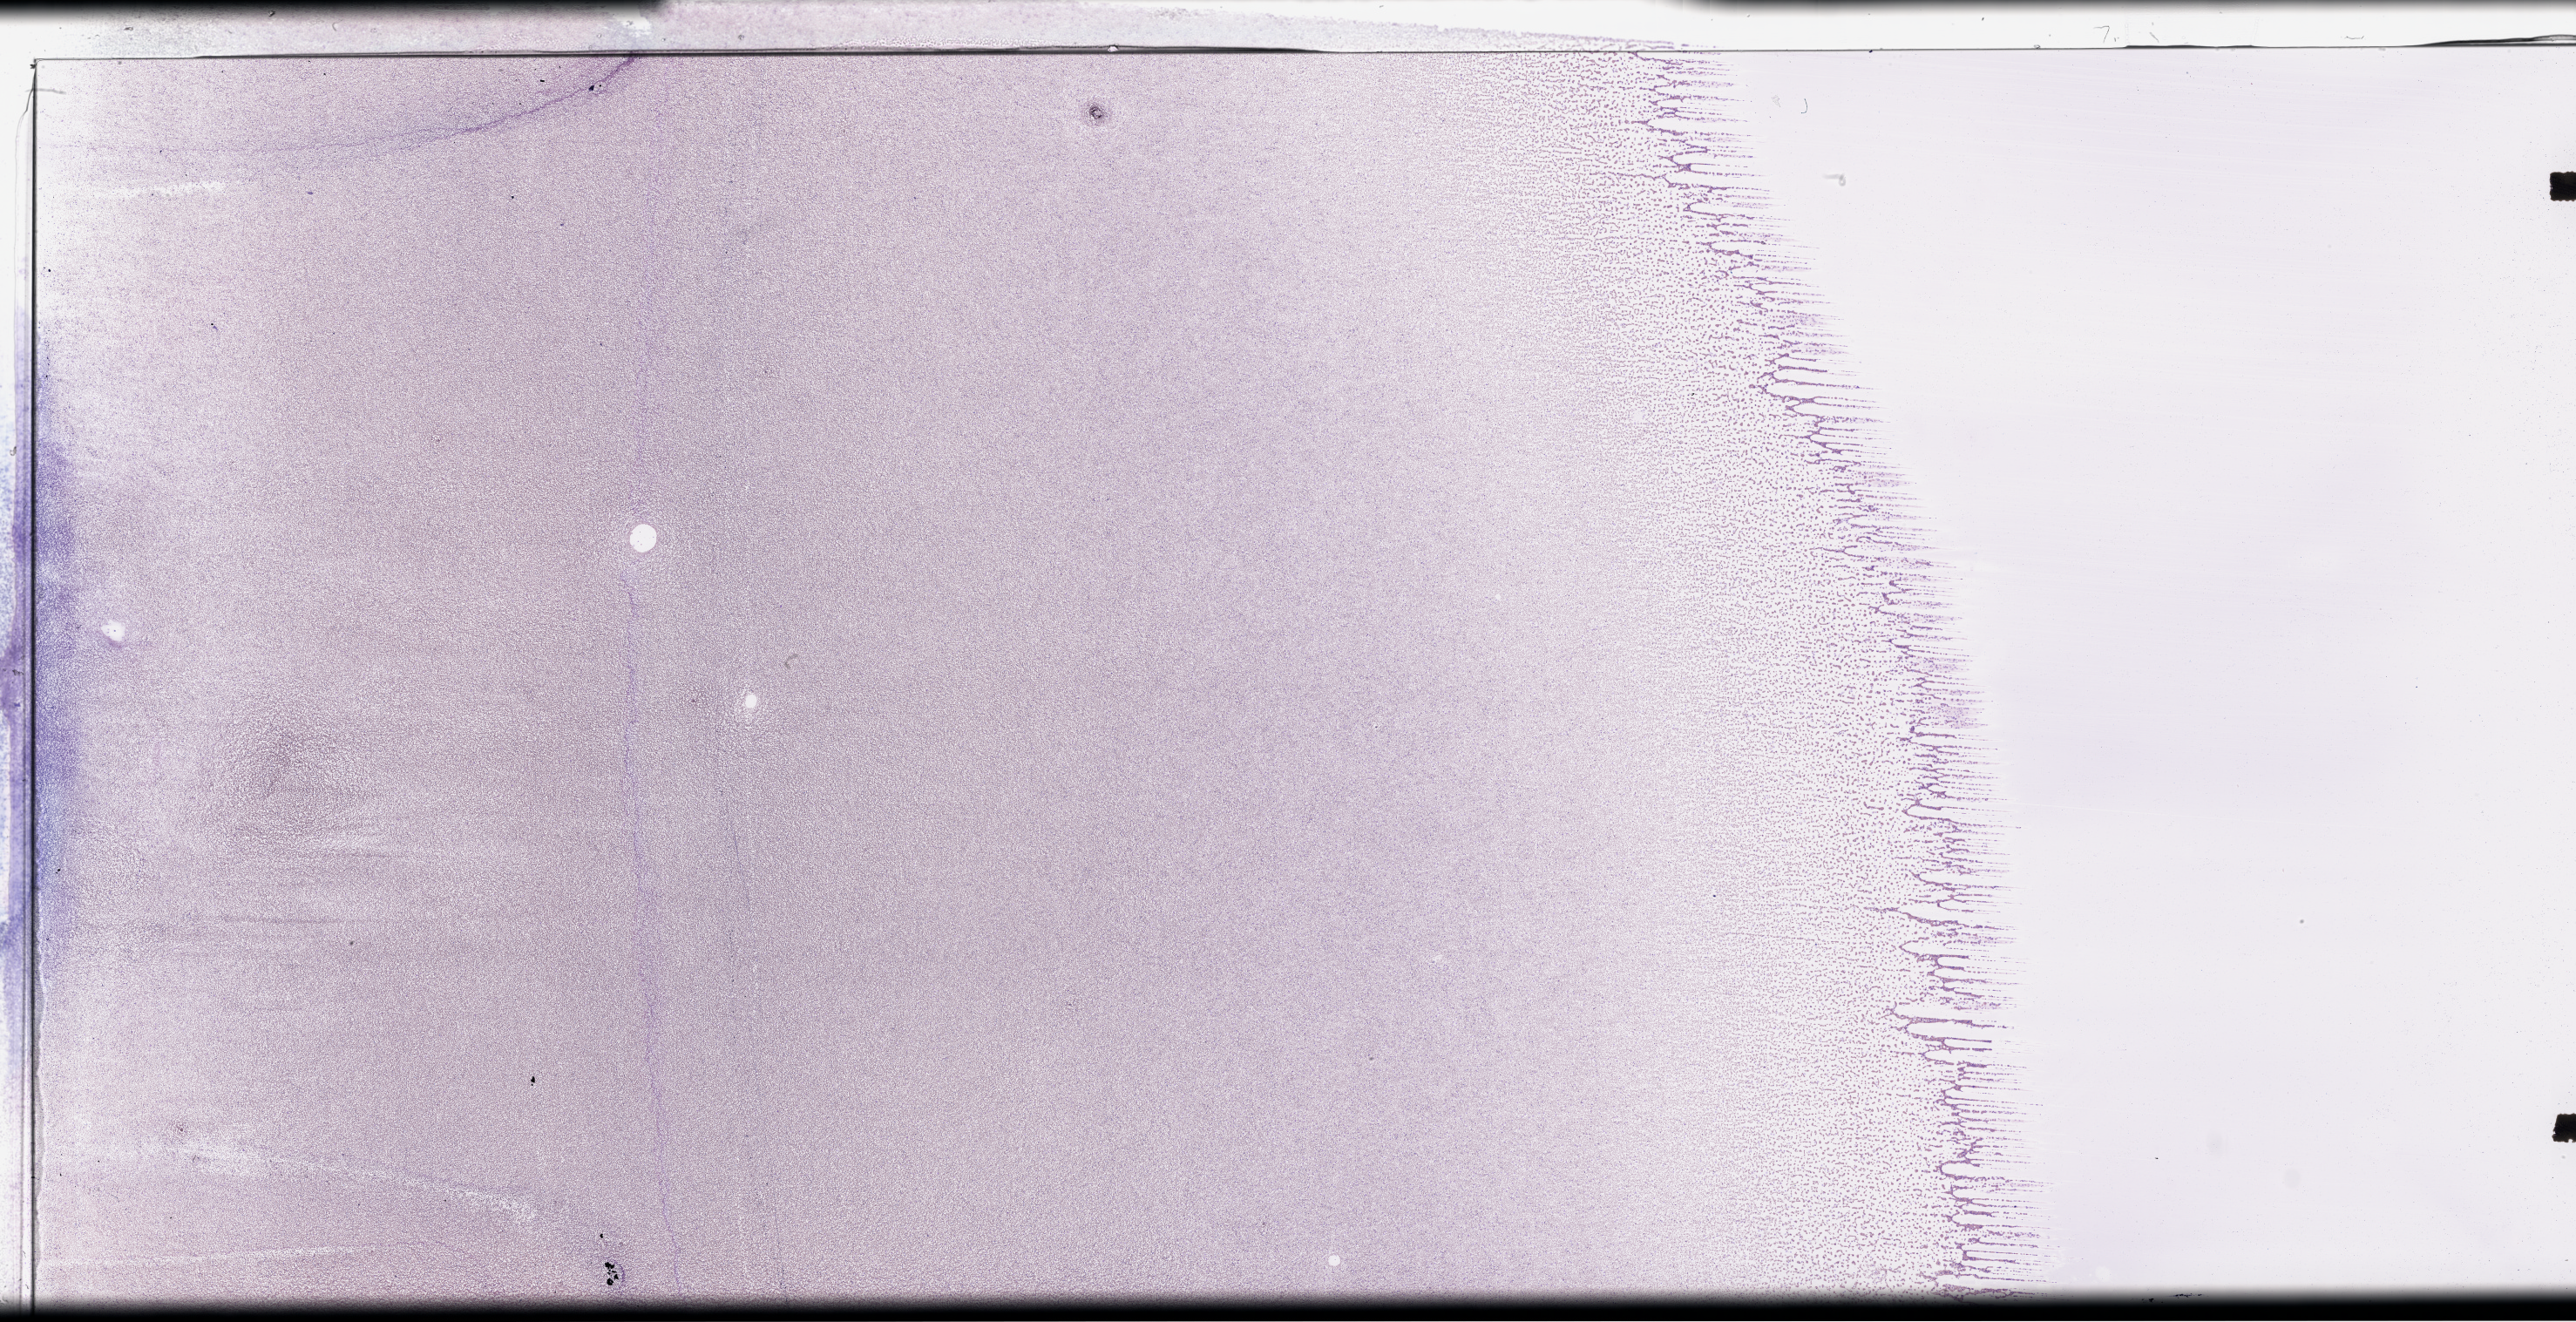
Whole-slide histology image, H&E-stained, low-resolution overview of the scanned area, about 47.7 x 24.5 mm (acquisition: 40x scan), peripheral blood (leukaemic) sample. Patient: male, age 19 years.
FAB classification: M1. WHO classification: AML with myelodysplasia-related changes. Diagnosis: Acute Myeloid Leukemia.